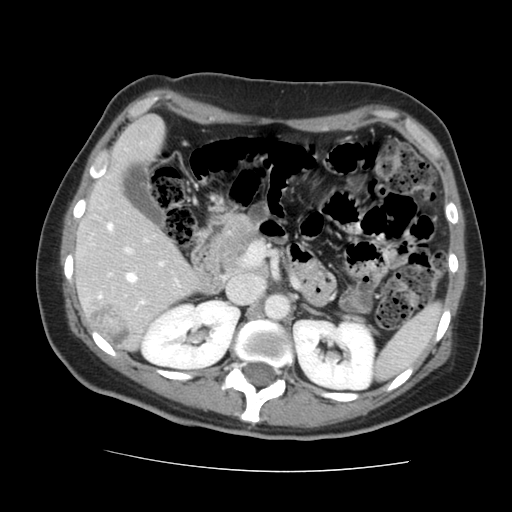
Contrast-enhanced abdominal CT, one axial slice; position 82 of 144 along the scan axis; 120 kVp; intravenous contrast given; soft-tissue window (W 400 / L 40 HU); 2.5 mm slice thickness; 512 × 512 image matrix, field of view 333 × 333 mm. Female patient, age 46 years. Case-level facts recorded for this patient, not image findings: diagnosis: colorectal cancer liver metastases, imaged before liver resection; multiple liver metastases: no; largest metastasis: 2.8 cm; disease in both lobes: no.
Structures marked on this image (manually delineated by an expert):
- hepatic veins: box from (x=126, y=273) to (x=137, y=282) px
- liver: (x=78, y=118)–(x=197, y=348)
- planned liver remnant (the part of the liver to remain after resection): (x=78, y=118)–(x=197, y=337)
- portal vein (with intrahepatic branches): (x=99, y=224)–(x=164, y=311)
- liver metastasis: (x=90, y=303)–(x=132, y=347)